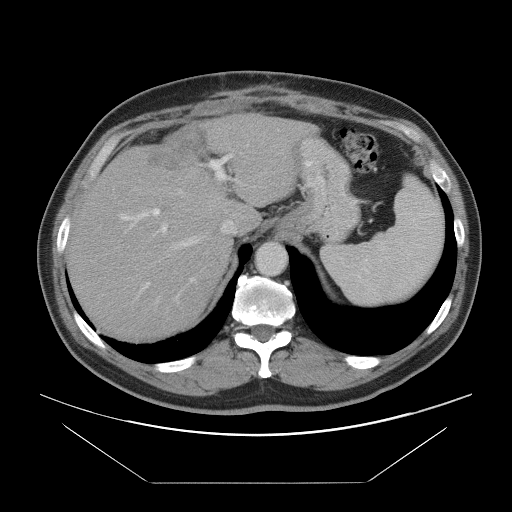
Contrast-enhanced abdominal CT, one axial slice. Position 68 of 97 along the scan axis. 120 kVp. Intravenous contrast given. Soft-tissue window (W 400 / L 40 HU). 5 mm slice thickness. 512 × 512 image matrix, field of view 442 × 442 mm. Male patient, age 62 years. From the clinical record (not read from this slice): diagnosis: colorectal cancer liver metastases, imaged before liver resection; multiple liver metastases: no; largest metastasis: 7 cm.
Outlined on this slice (expert manual segmentation):
- hepatic veins: box from (x=167, y=139) to (x=285, y=257) px
- liver: (x=71, y=113)–(x=305, y=339)
- planned liver remnant (the part of the liver to remain after resection): (x=71, y=170)–(x=232, y=338)
- portal vein (with intrahepatic branches): (x=119, y=145)–(x=248, y=295)
- liver metastasis: (x=150, y=129)–(x=209, y=171)